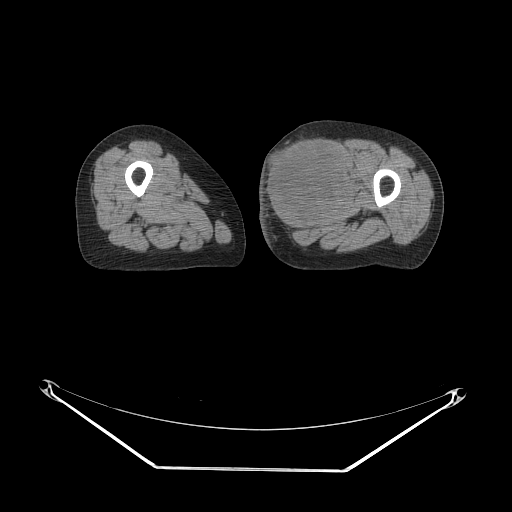
CT of an extremity soft-tissue mass (from a PET/CT study), one axial slice; position 34 of 91 along the scan axis; soft-tissue window (W 400 / L 40 HU); 3.75 mm slice thickness; 512 × 512 image matrix, field of view 500 × 500 mm. Female patient. Case-level facts recorded for this patient, not image findings: histological type: pleomorphic leiomyosarcoma; grade: high; site of the primary tumour: left thigh.
Outlined on this slice (expert contour drawn on MRI and transferred to this co-registered scan by the dataset authors):
- gross tumour volume including surrounding oedema: bounding box (x1, y1, x2, y2) in pixels: (263, 135, 357, 234)
- gross tumour volume (mass): (263, 135, 353, 232)